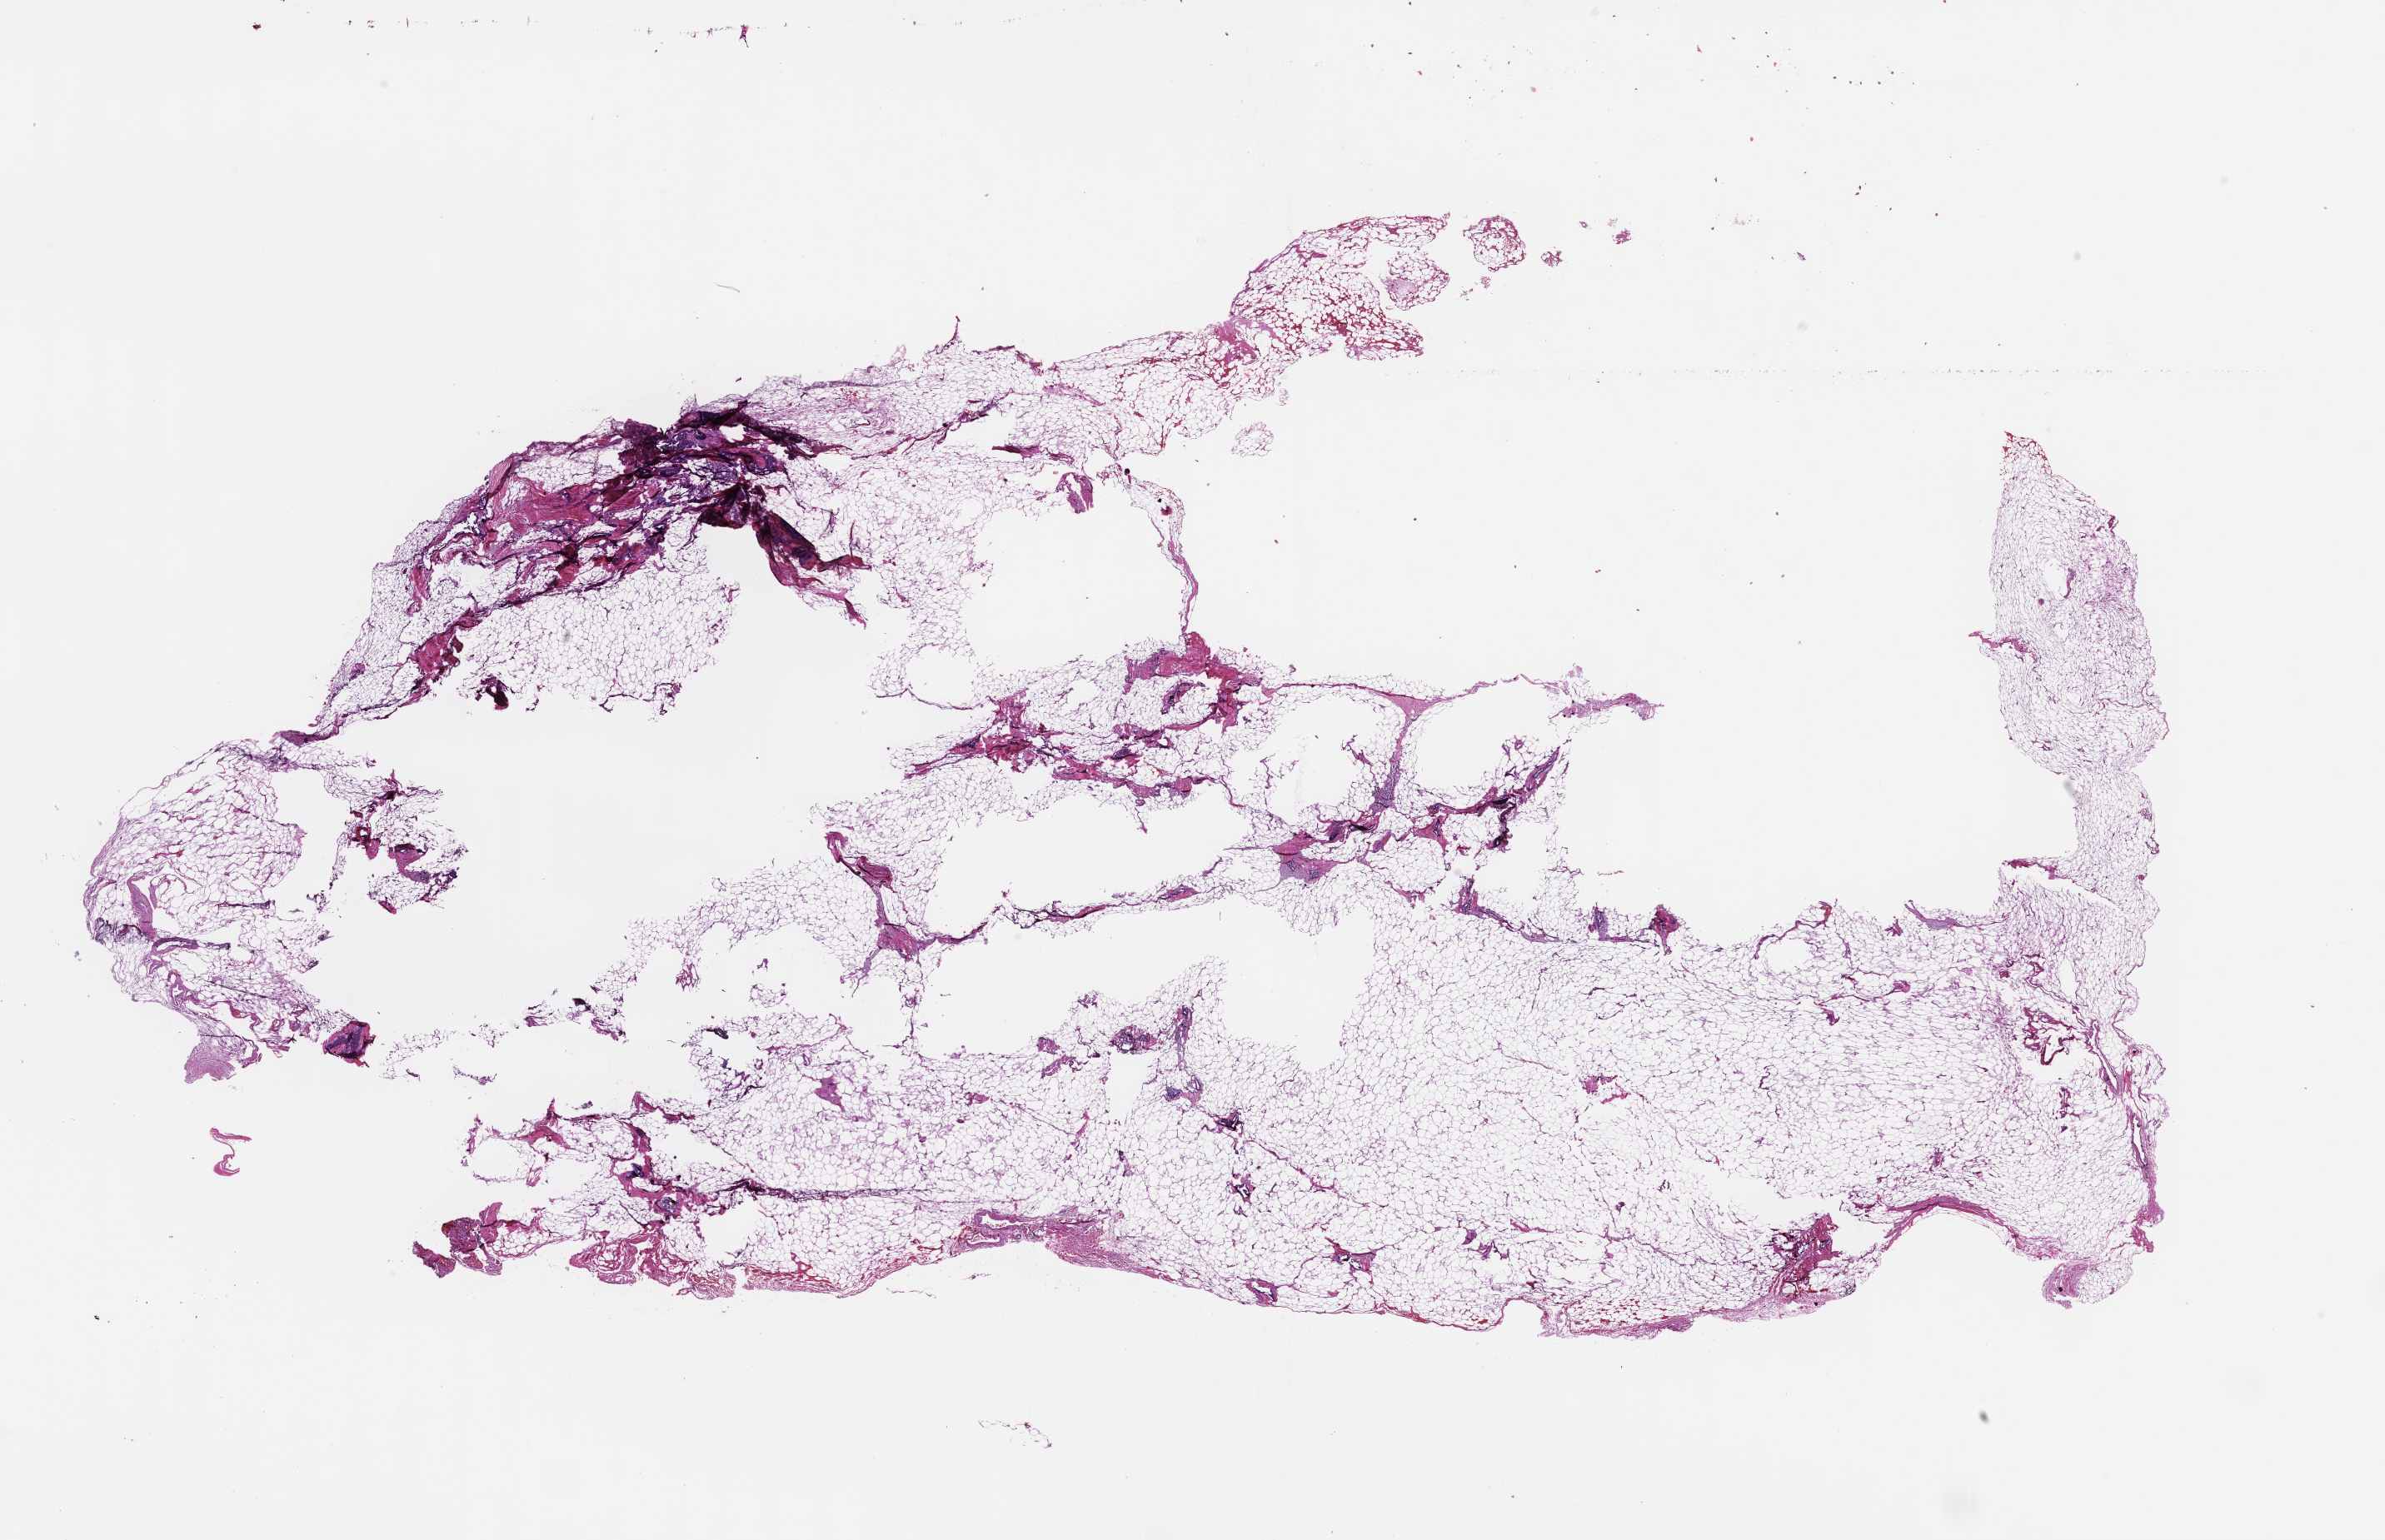
Haematoxylin and eosin whole-slide image — shown as a low-resolution overview of the whole scanned area (about 23.1 x 14.9 mm). FFPE section. Specimen time point: collected at baseline (before treatment). Patient: female.
* this section: metastatic tumor tissue
* patient diagnosis (primary): Ovarian Carcinoma